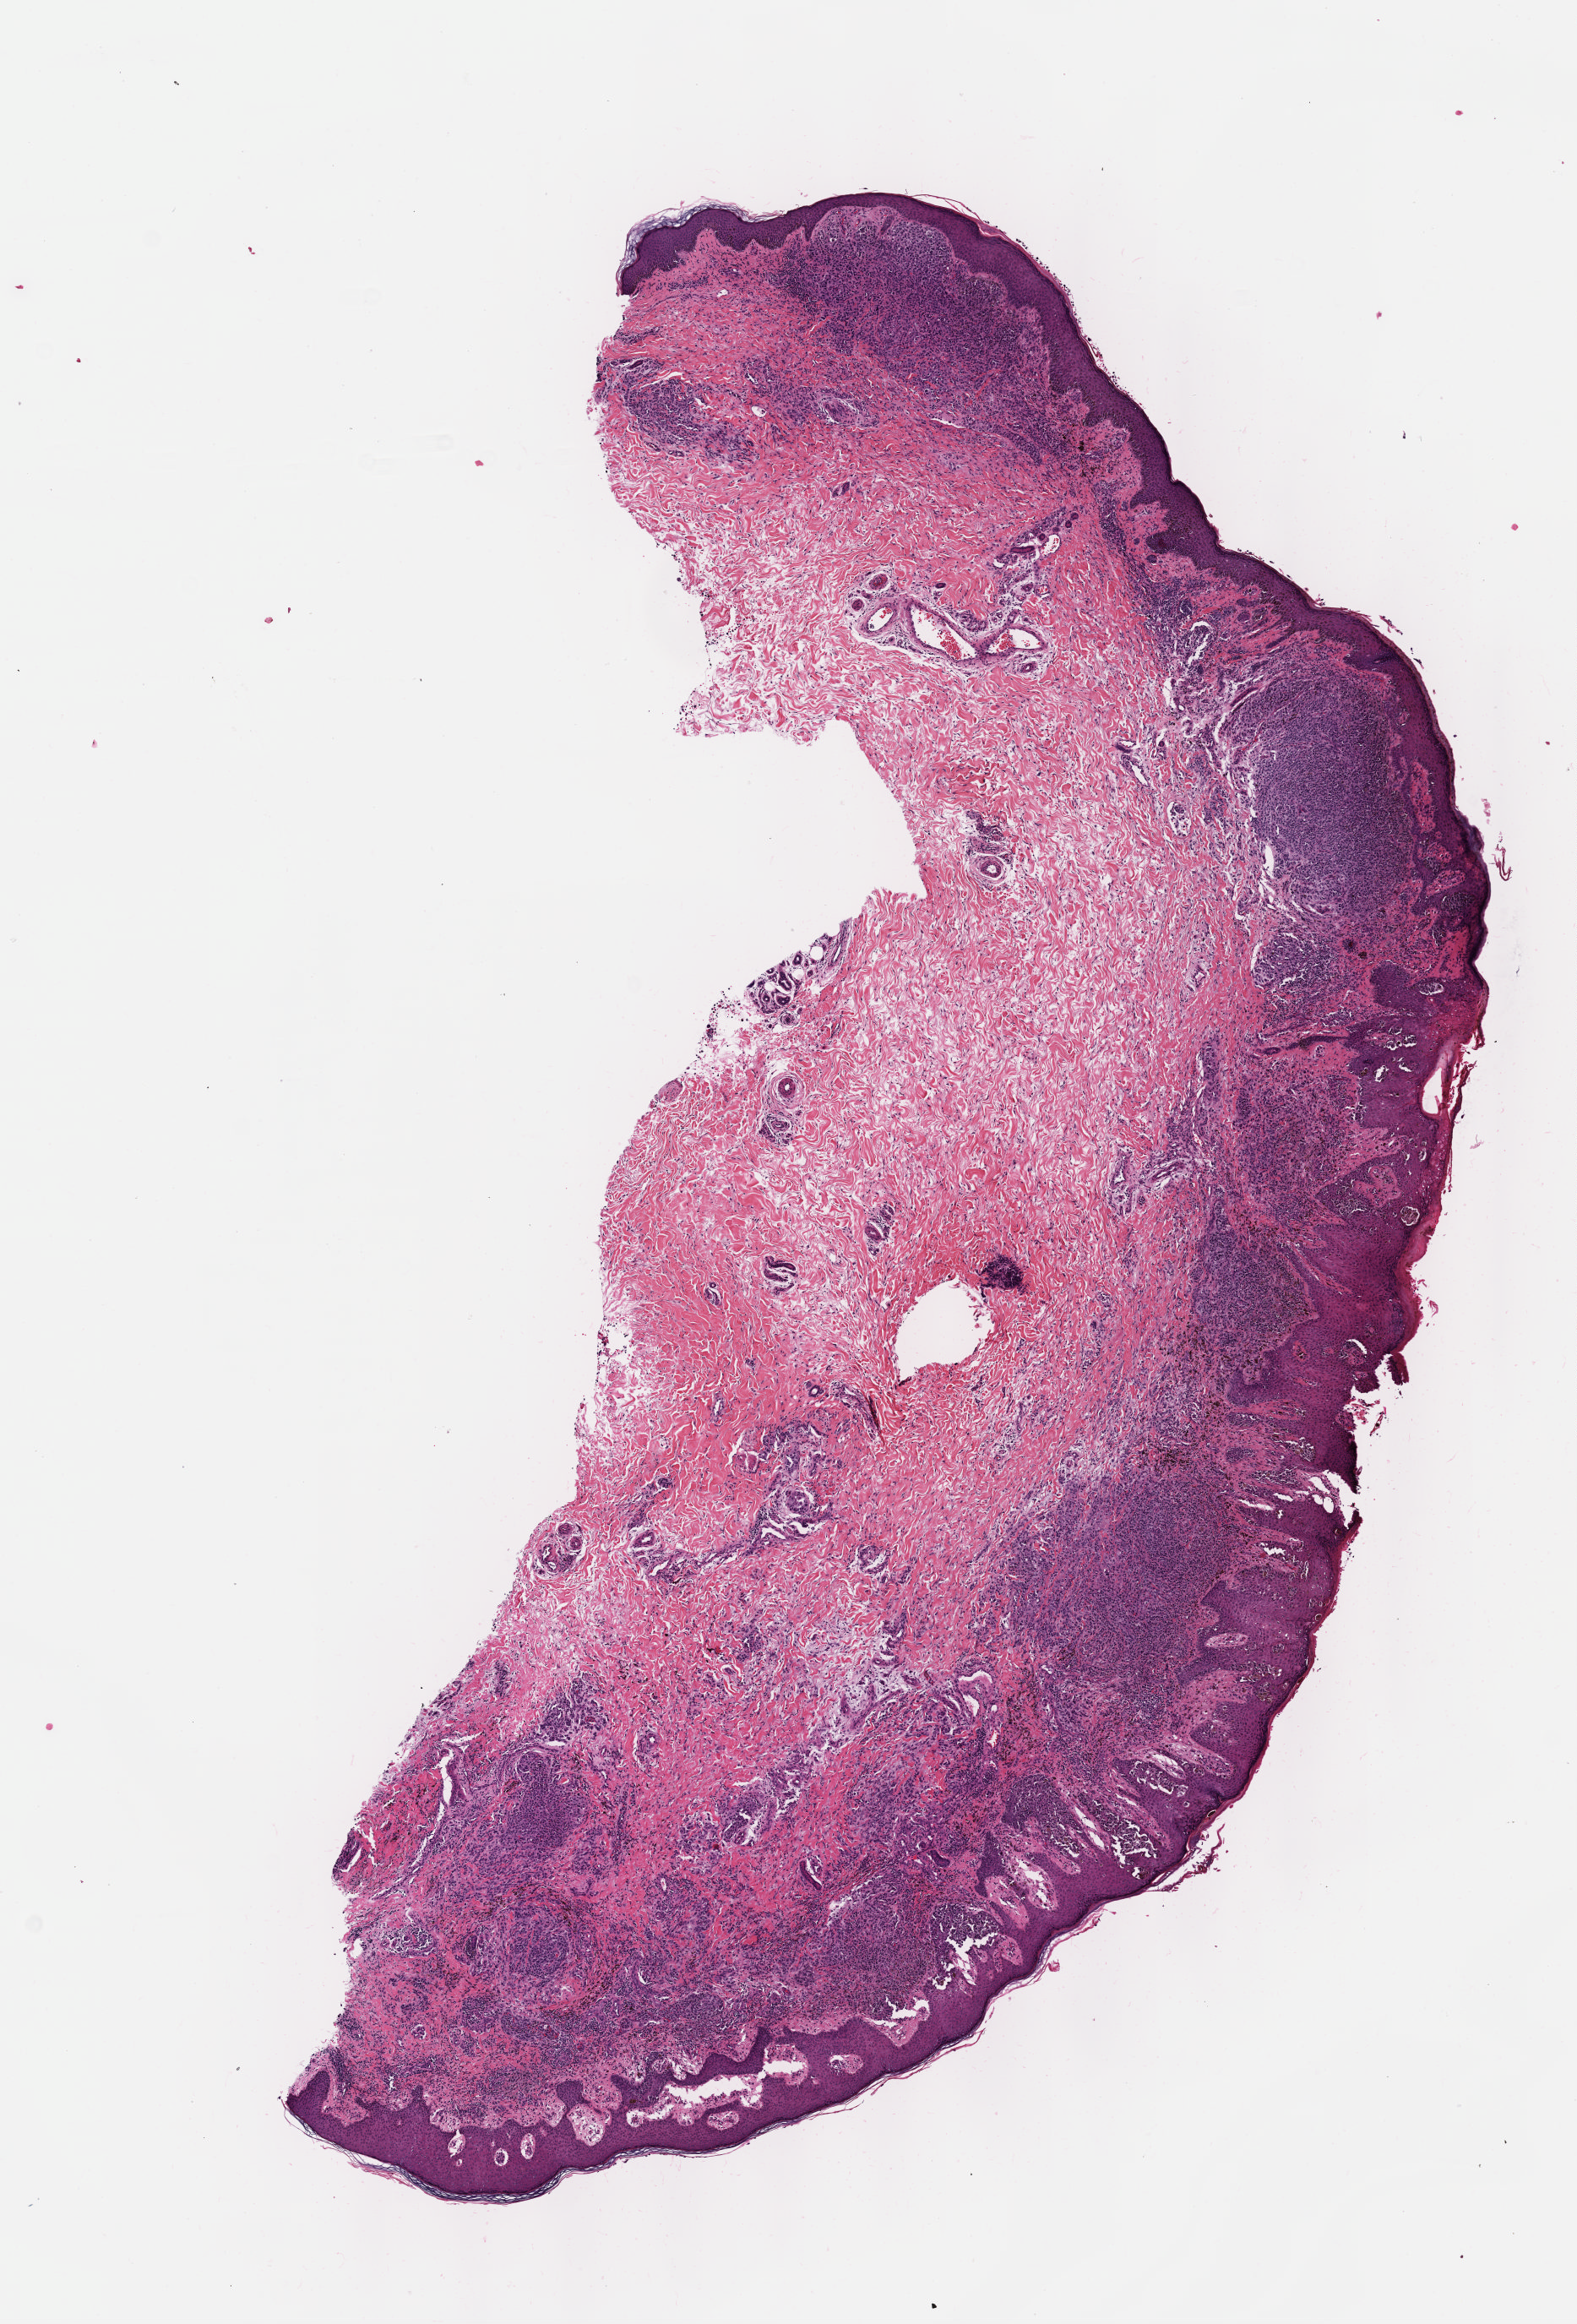
Digitized H&E tissue section (whole slide), whole scanned area (about 7.5 x 11.1 mm, slide scanned at 40x) shown as a low-resolution overview. Formalin-fixed paraffin-embedded (FFPE) diagnostic section. Primary tumour sample from the skin. Patient: female, age at initial diagnosis 81 years.
AJCC pathologic stage: IIIC. TNM: T3b N3 M0. Diagnosis: Malignant melanoma, NOS.